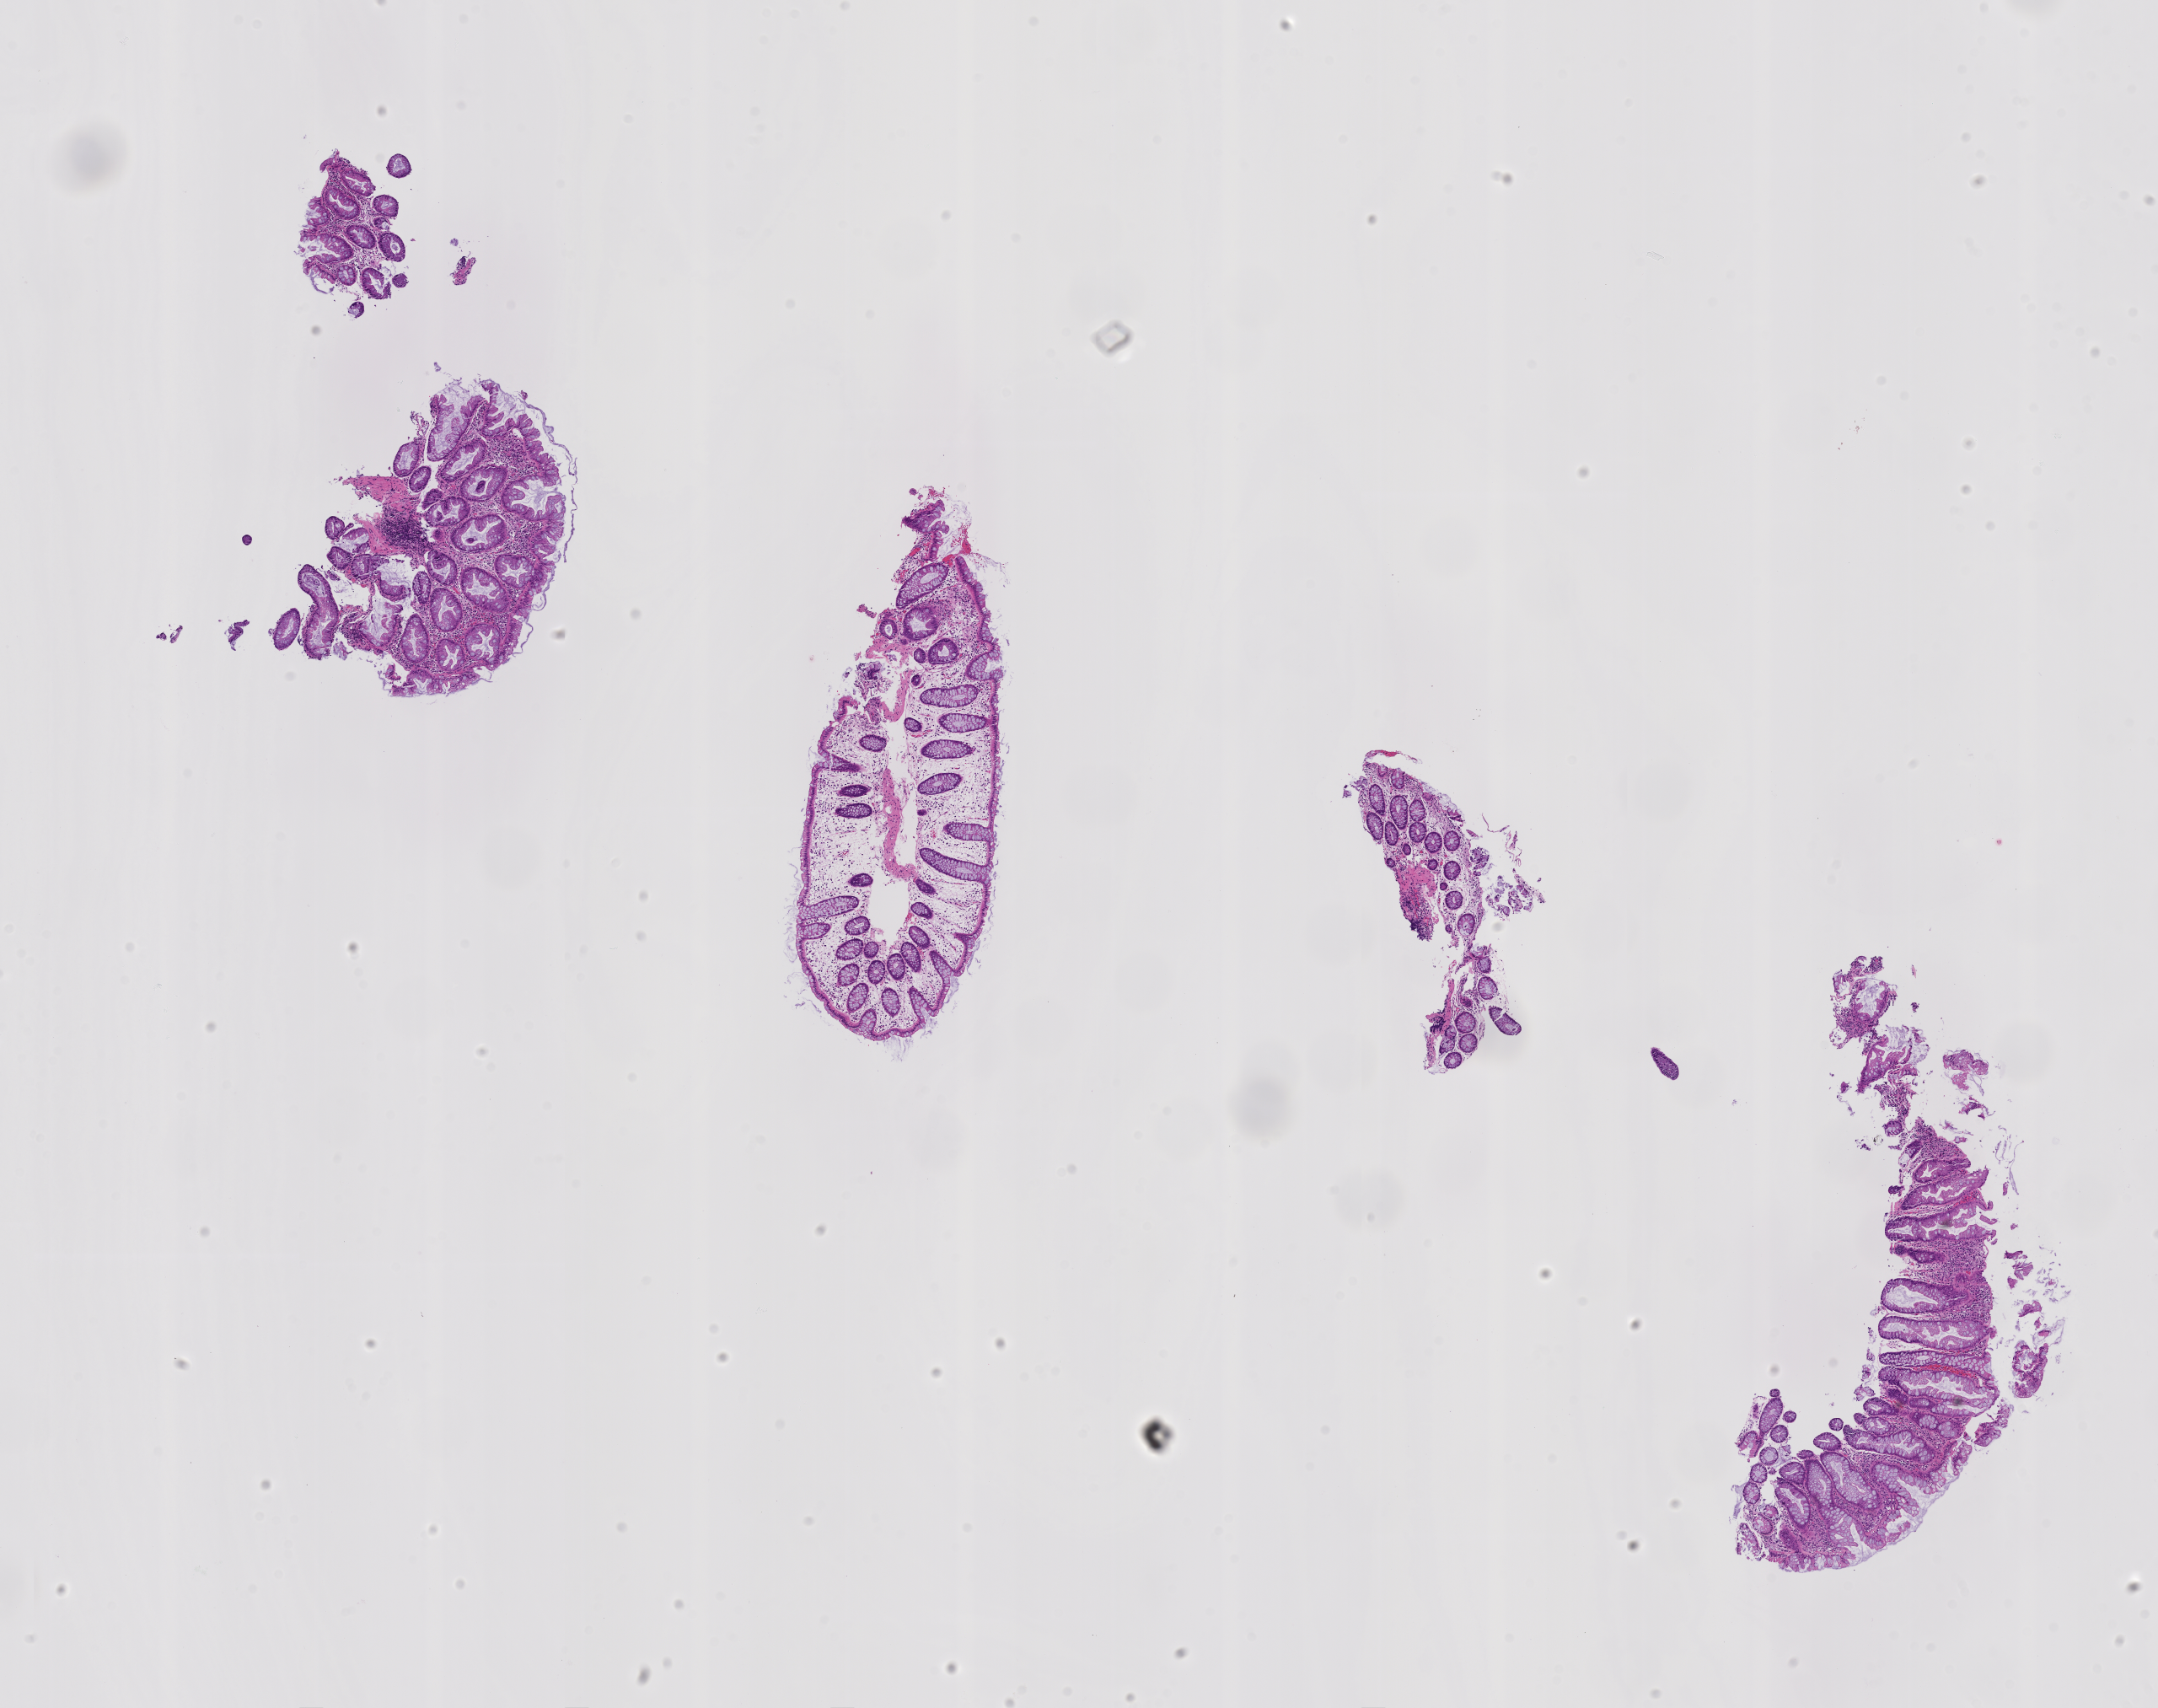
H&E whole-slide image of a colon biopsy, a low-resolution overview of the entire scanned area, about 10.2 x 8.1 mm. FFPE section. Descending colon. Patient sex: male.
Lesion category (as recorded): premalignant.